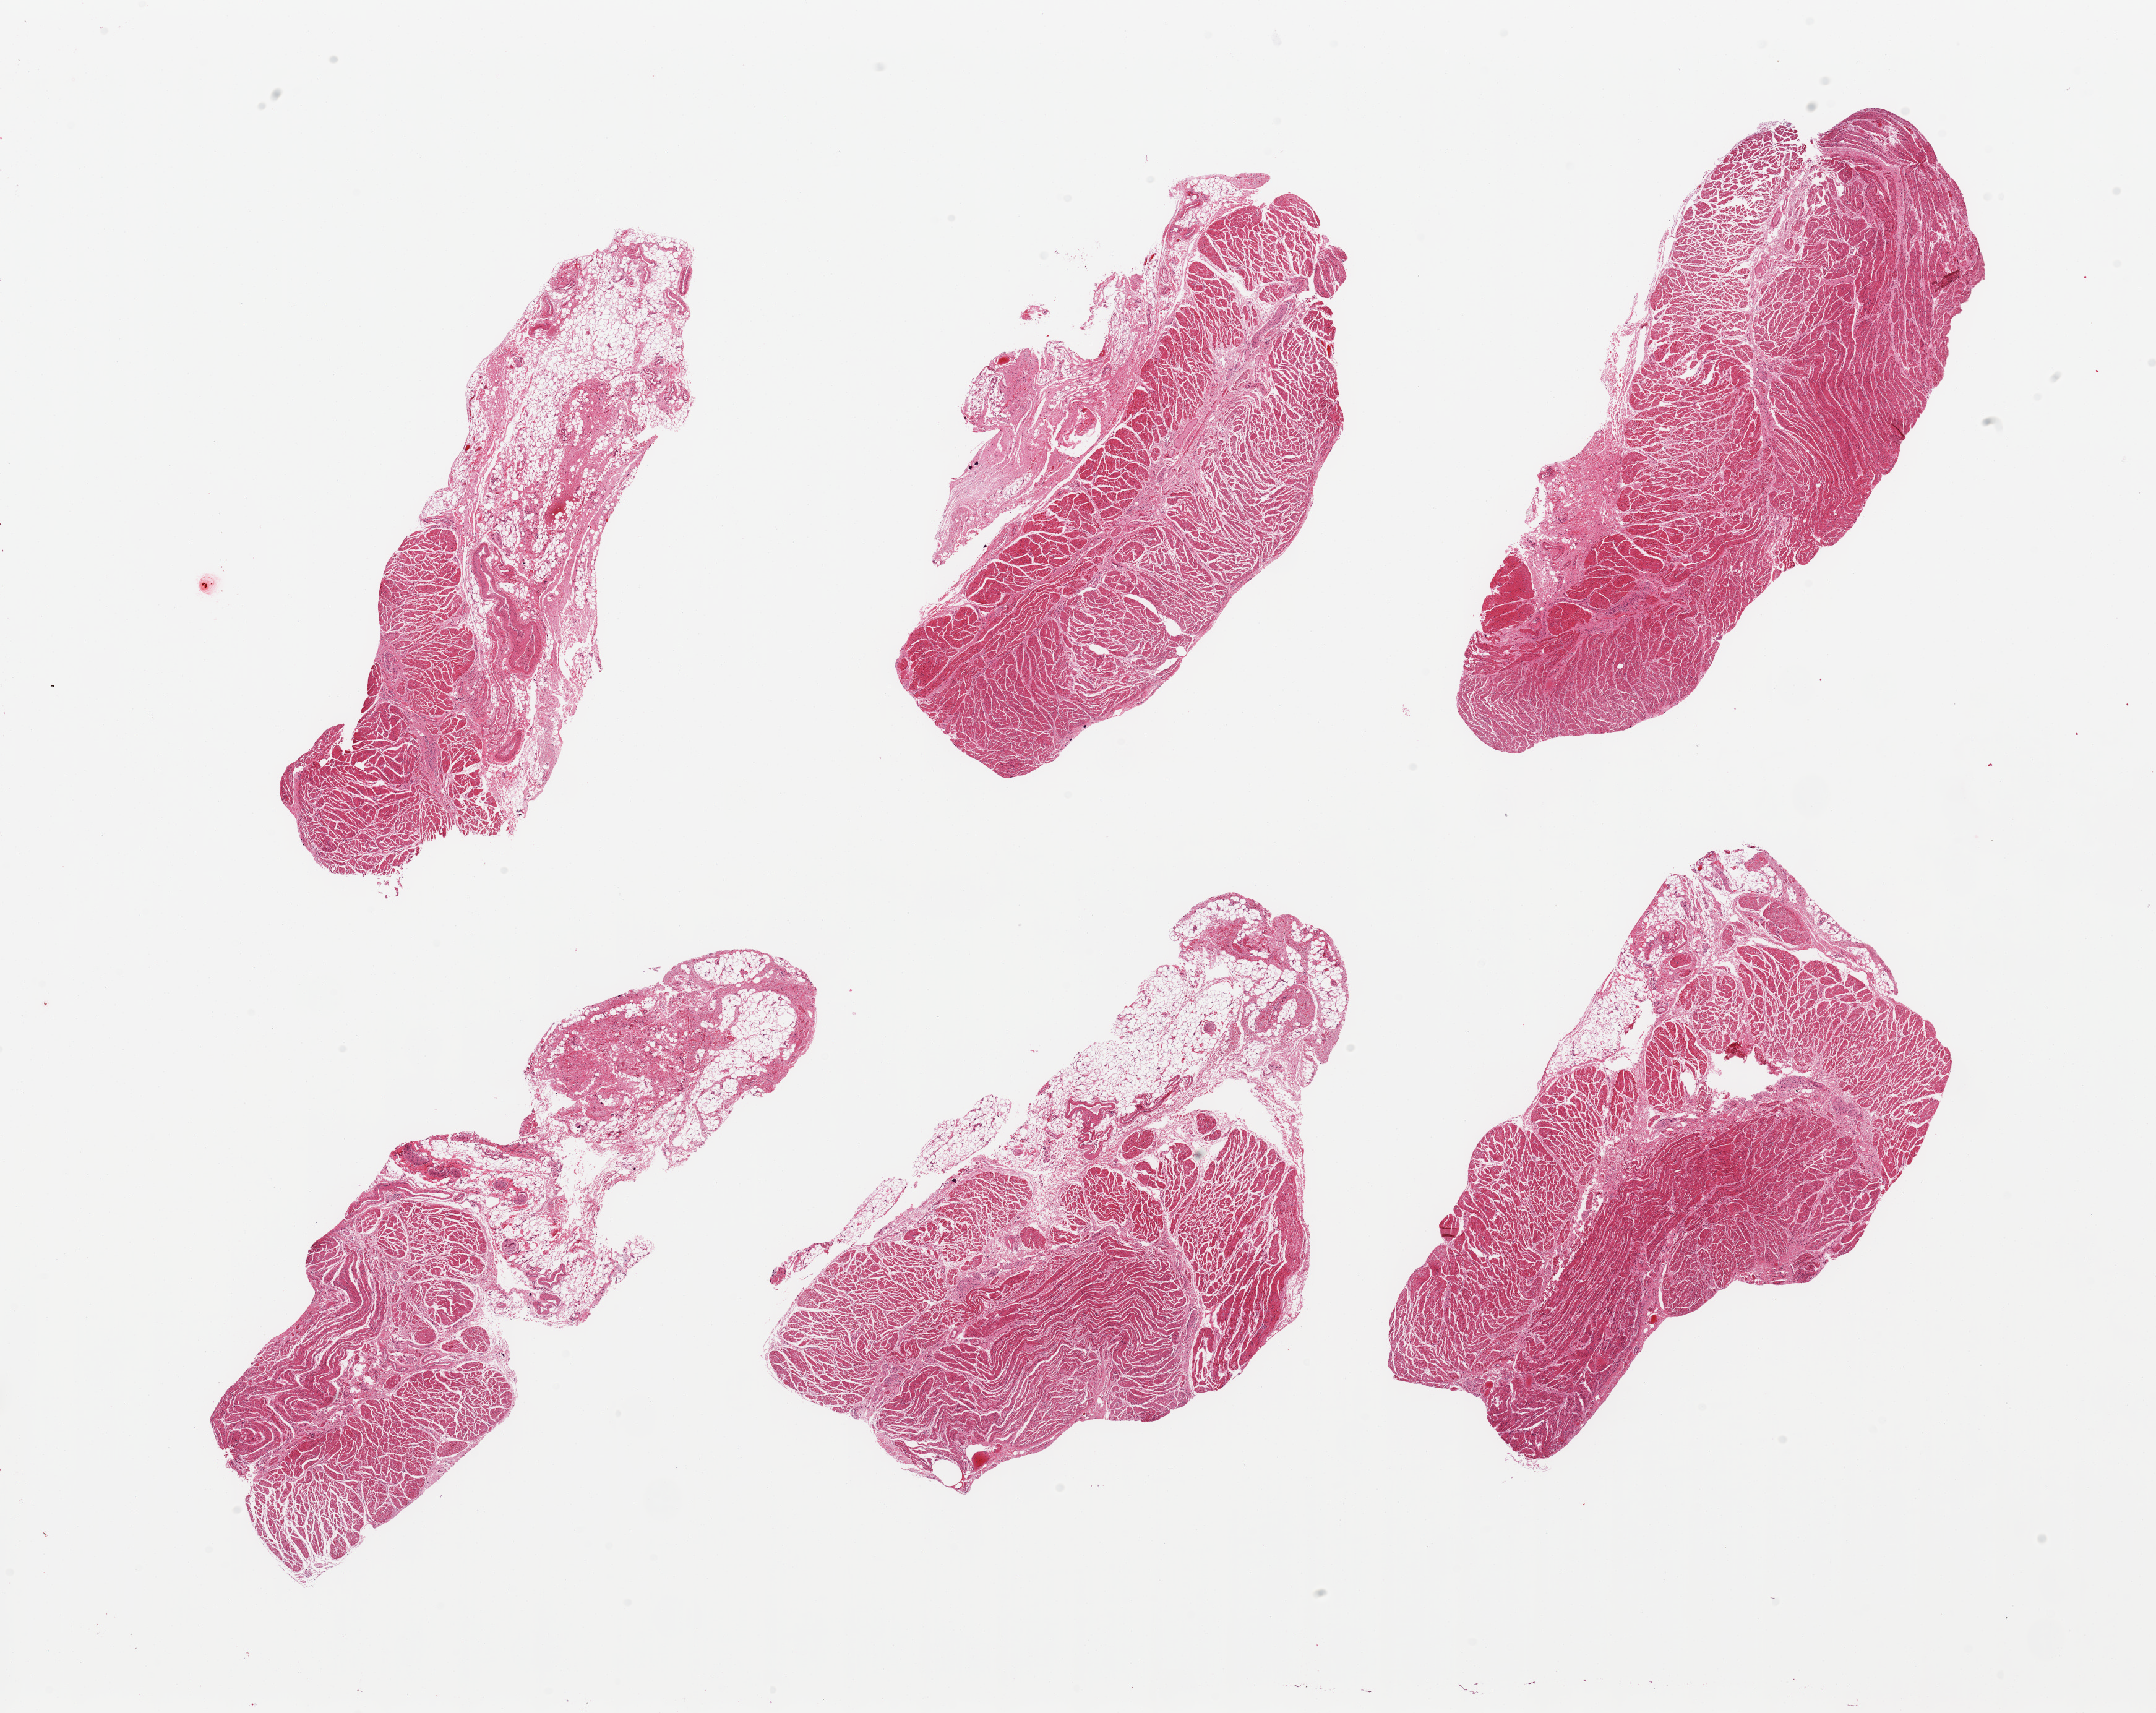
Haematoxylin and eosin whole-slide image — a low-resolution overview of the entire scanned area, about 27.6 x 21.9 mm (acquisition: 20x scan). PAXgene-fixed paraffin-embedded (PFPE) section. Target tissue: gastroesophageal junction. Tissue donor sample. Male donor.
* pathologist's review note for this sample: 6 pieces; up to 40% fat content